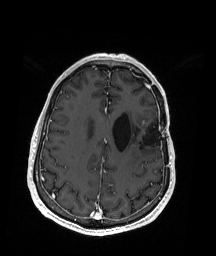
Brain MRI from a brain-tumour surgery series, one axial slice. Position 65 of 192 along the scan axis. T1-weighted post-contrast. 1 mm slice thickness. 216 × 256 image matrix, field of view 211 × 250 mm. From the clinical record (not read from this slice): histopathology: Oligodendroglioma; WHO grade: 2; IDH mutation: yes; tumour location: Left Insular.
Annotated regions visible in this slice (outlined manually by an expert reader):
- previous resection cavity: bounding box <132,123,156,146> (left, top, right, bottom; pixels)